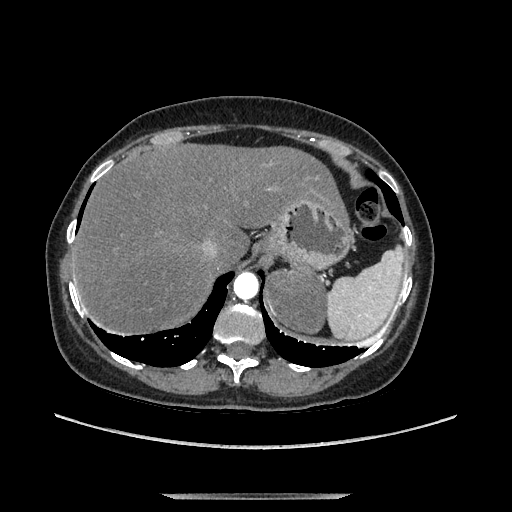
Contrast-enhanced abdominal CT, one axial slice. Soft-tissue window (W 400 / L 40 HU). 1.25 mm slice thickness. 512 × 512 image matrix. Female patient. Case-level facts recorded for this patient, not image findings: diagnosis: adrenocortical carcinoma; tumour side: left adrenal; tumour size at pathology: 9 cm; Ki-67 index: 2 %; stage (as recorded): 3.
Annotated regions visible in this slice (semi-automatic segmentation, software-assisted and operator-edited):
- mass: box from (x=271, y=272) to (x=325, y=332) px